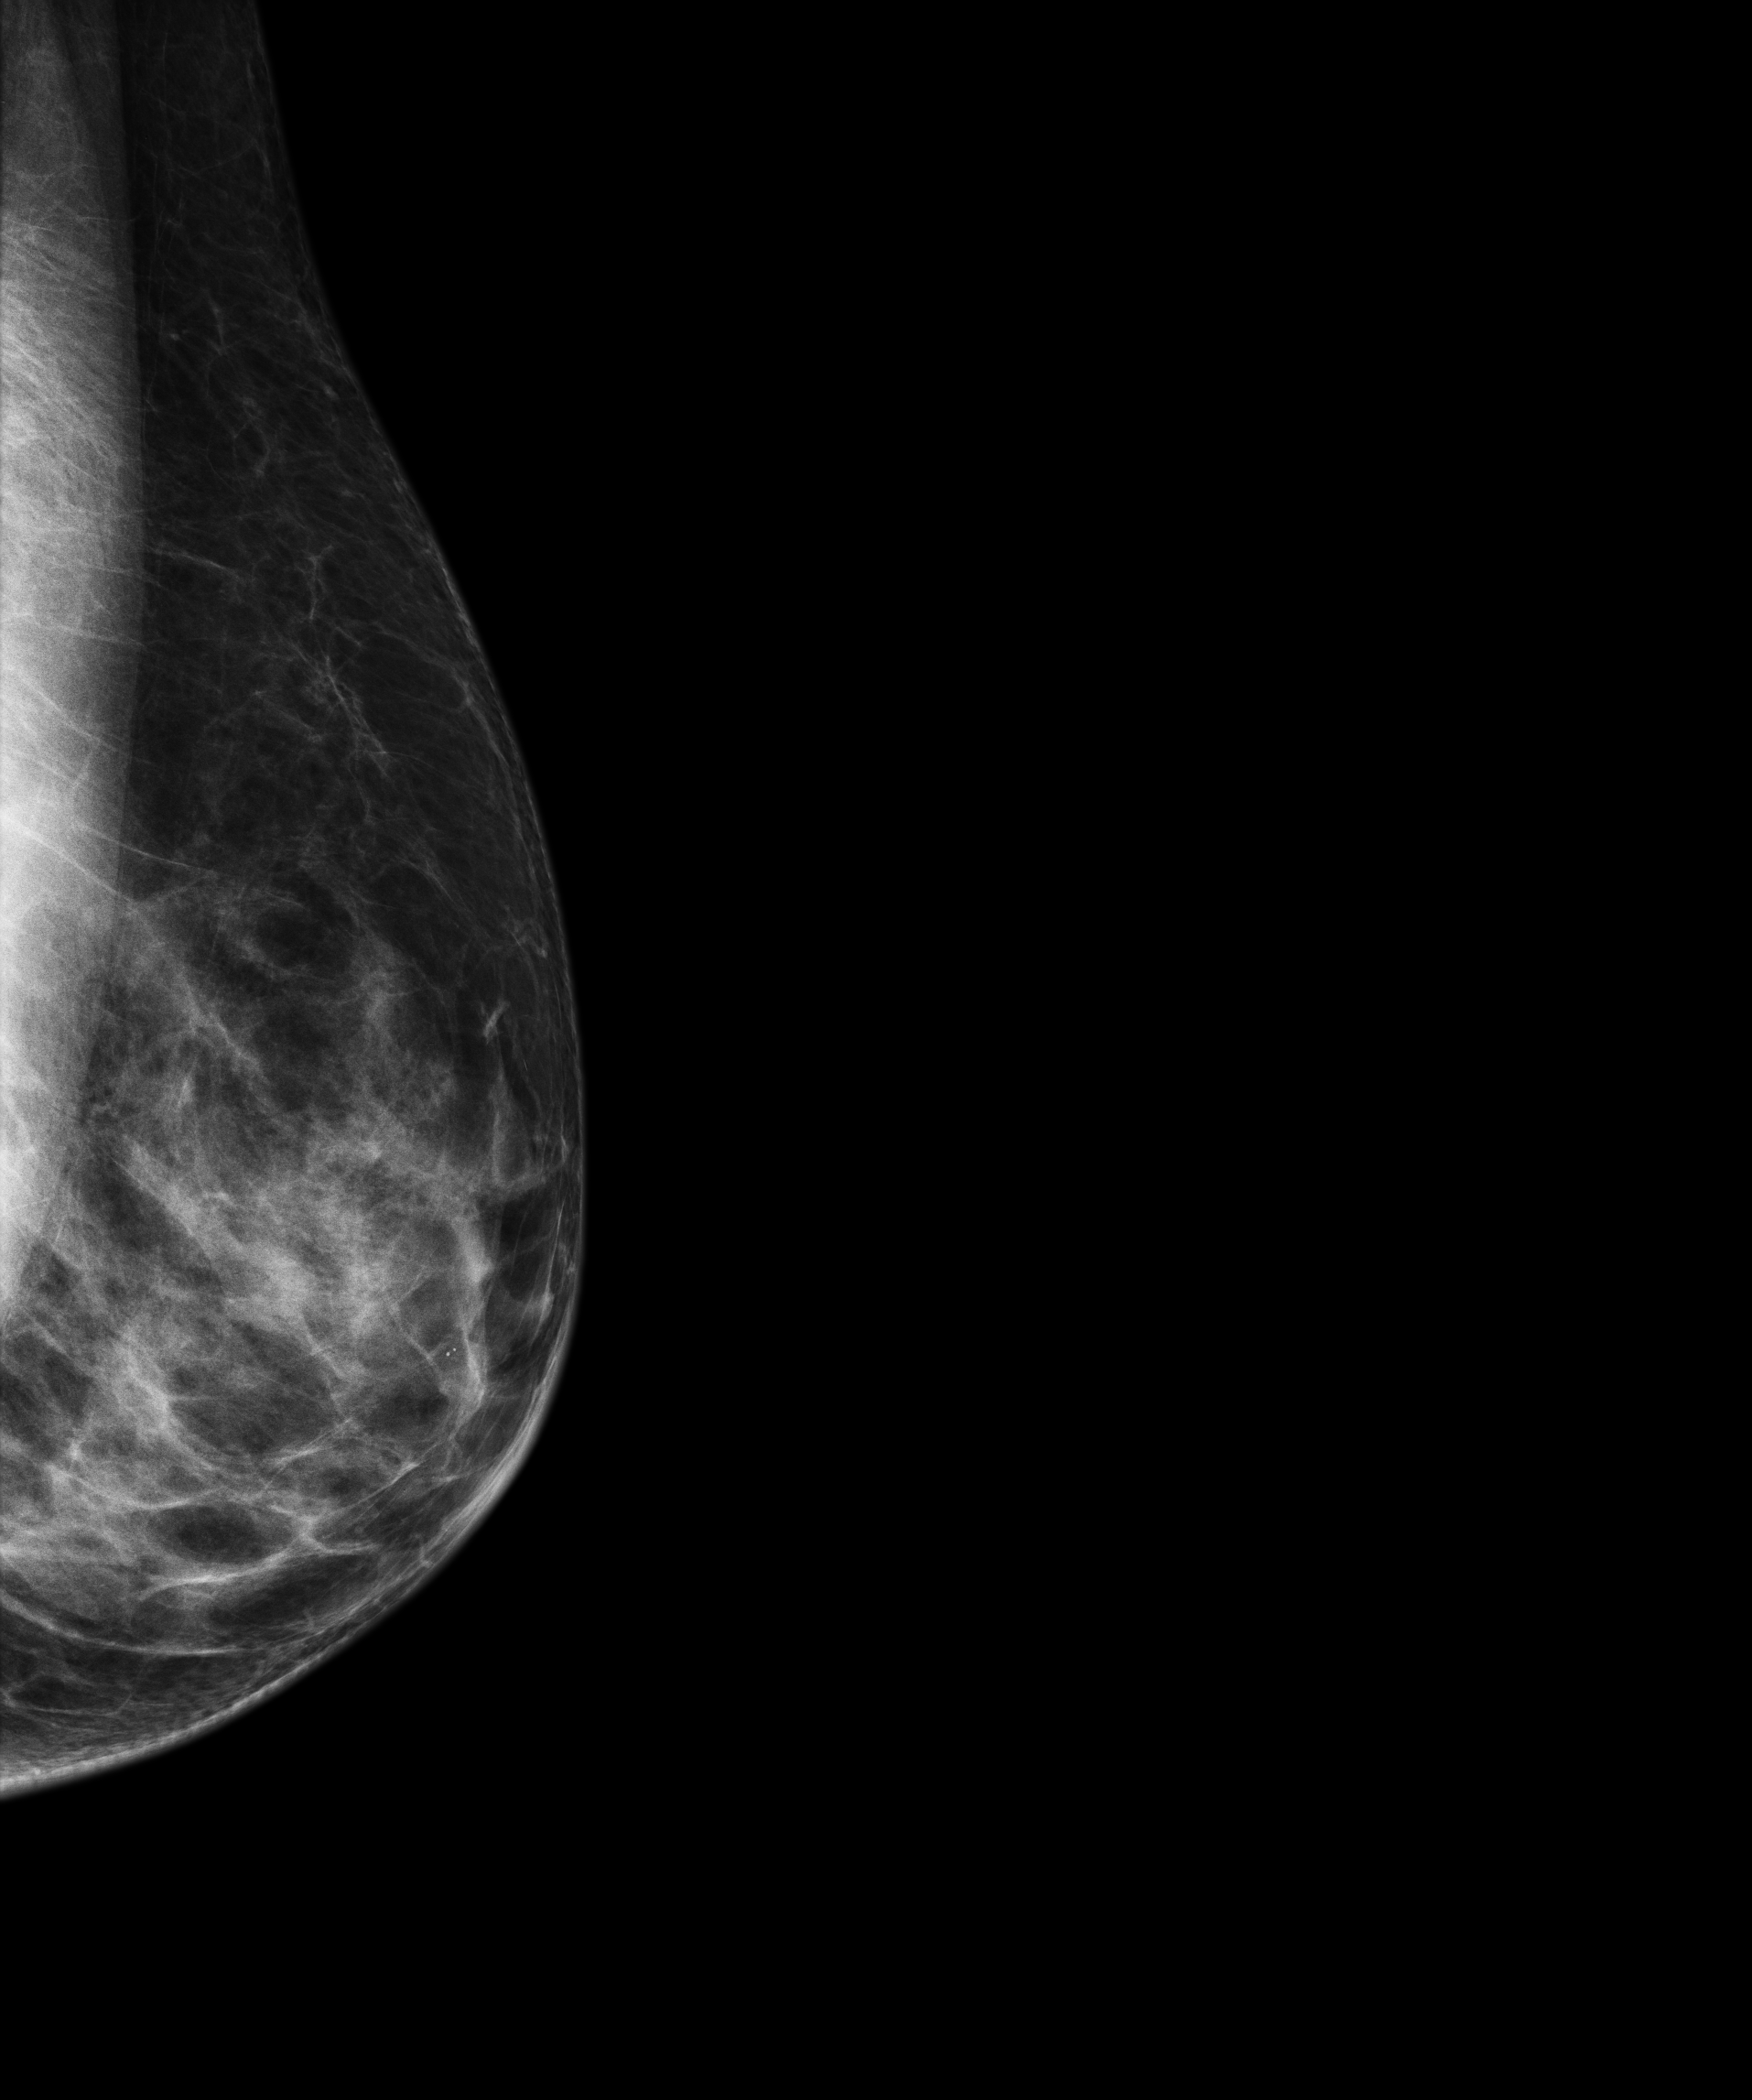
Digital mammogram (FFDM), left breast, exaggerated CC view (lateral), annual screening mammography examination, compressed breast thickness 55 mm, system: Senographe Essential ADS_56.21.3. Female patient, age 66 years.
- breast density at the screening exam (both breasts): heterogeneously dense (BI-RADS density category c)
- final BI-RADS assessment for this screening round (tomosynthesis exam, both breasts): category 1
- recall: no recall after this screen